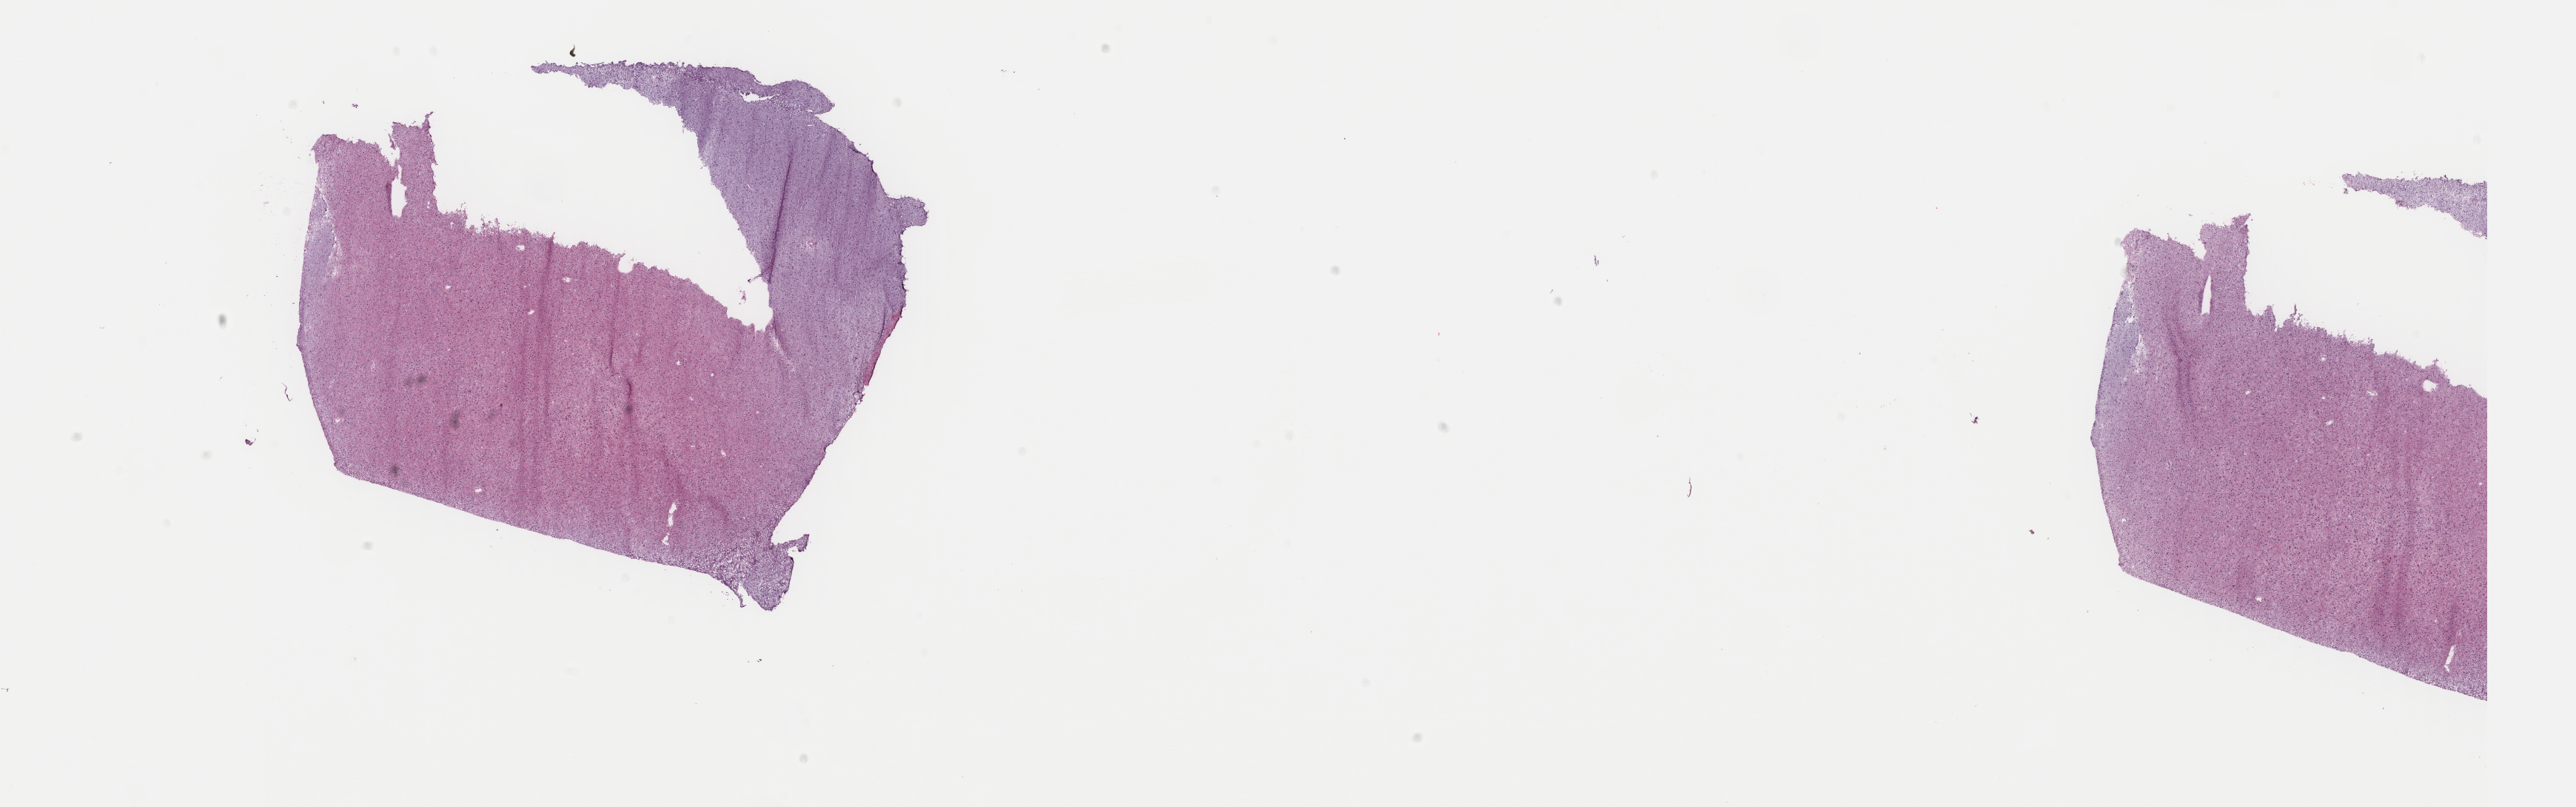
Digitized Hematoxylin and eosin (H&E) stained tissue section (whole slide), shown as a low-resolution overview of the whole scanned area (about 27.6 x 8.7 mm, from a 40x scan); frozen section; primary tumour sample from the brain. Male patient; age at initial diagnosis 38 years. Histologic grade: G2 (moderately differentiated). Slide review estimates, as recorded: tumour cells 35%, tumour nuclei 90%, normal cells 10%, stromal cells 55%, necrosis 0%. Infiltration values recorded for this section: lymphocyte infiltration 0%, monocyte infiltration 0%, neutrophil infiltration 0%.
Diagnosis: Mixed glioma (cerebrum).